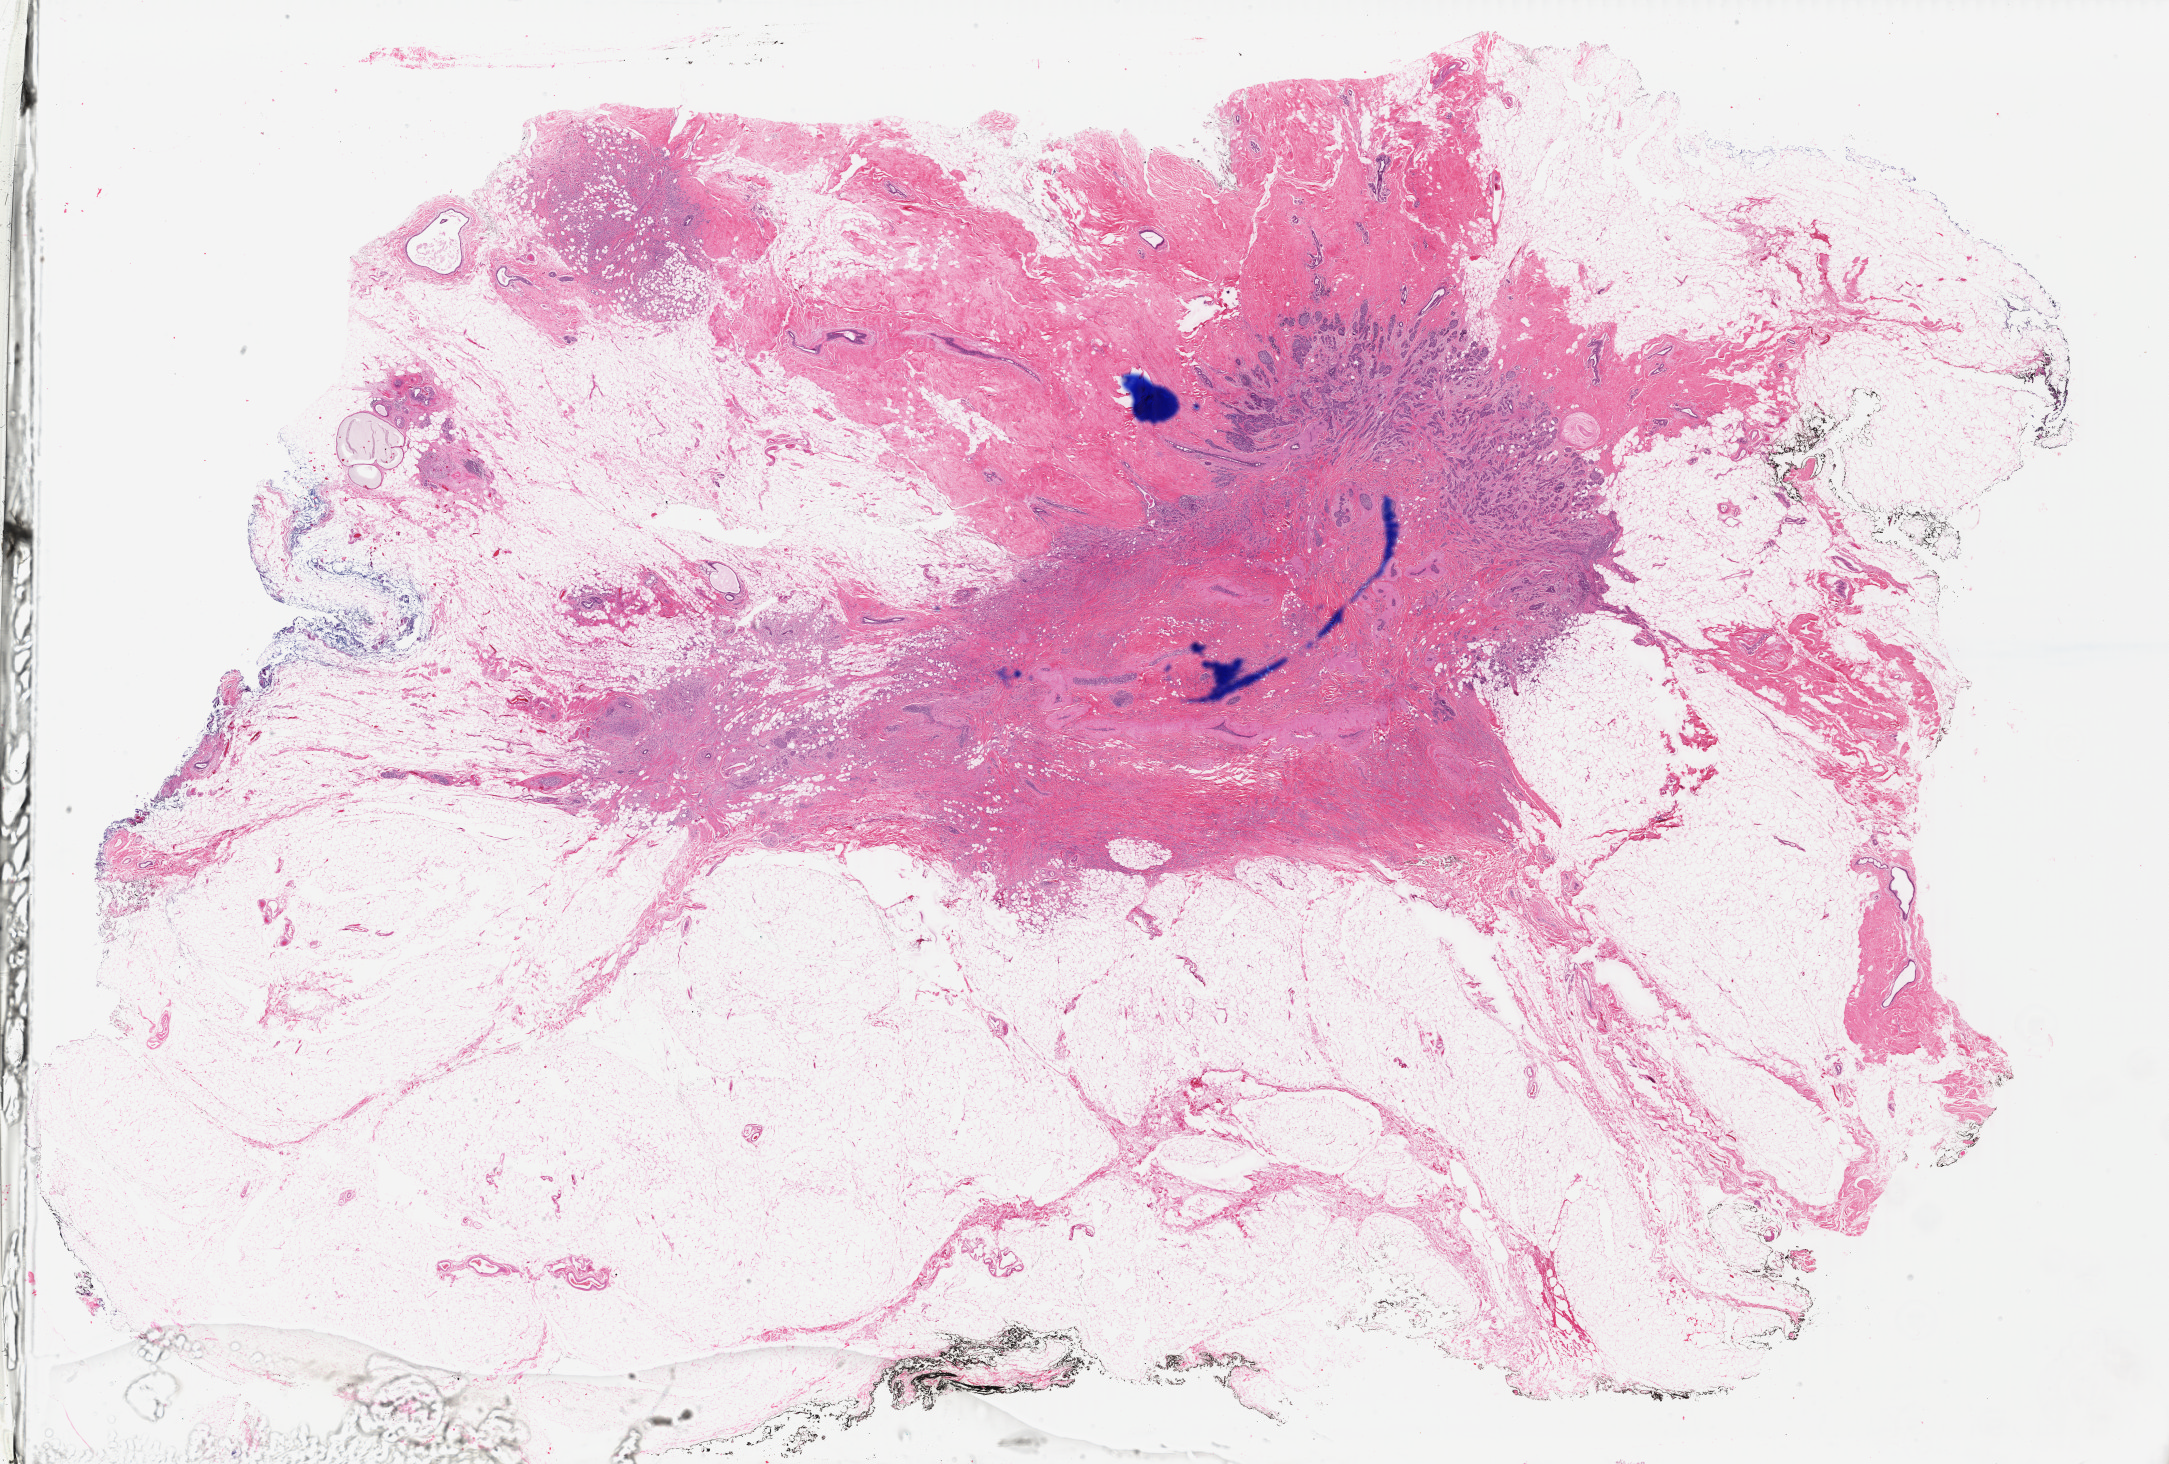
Digitized Hematoxylin and eosin (H&E) stained tissue section (whole slide) — a low-resolution overview of the entire scanned area, about 34.5 x 23.3 mm, FFPE section, breast, primary tumour sample. Female patient; age at initial diagnosis 62 years.
• histologic diagnosis: Infiltrating duct carcinoma, NOS